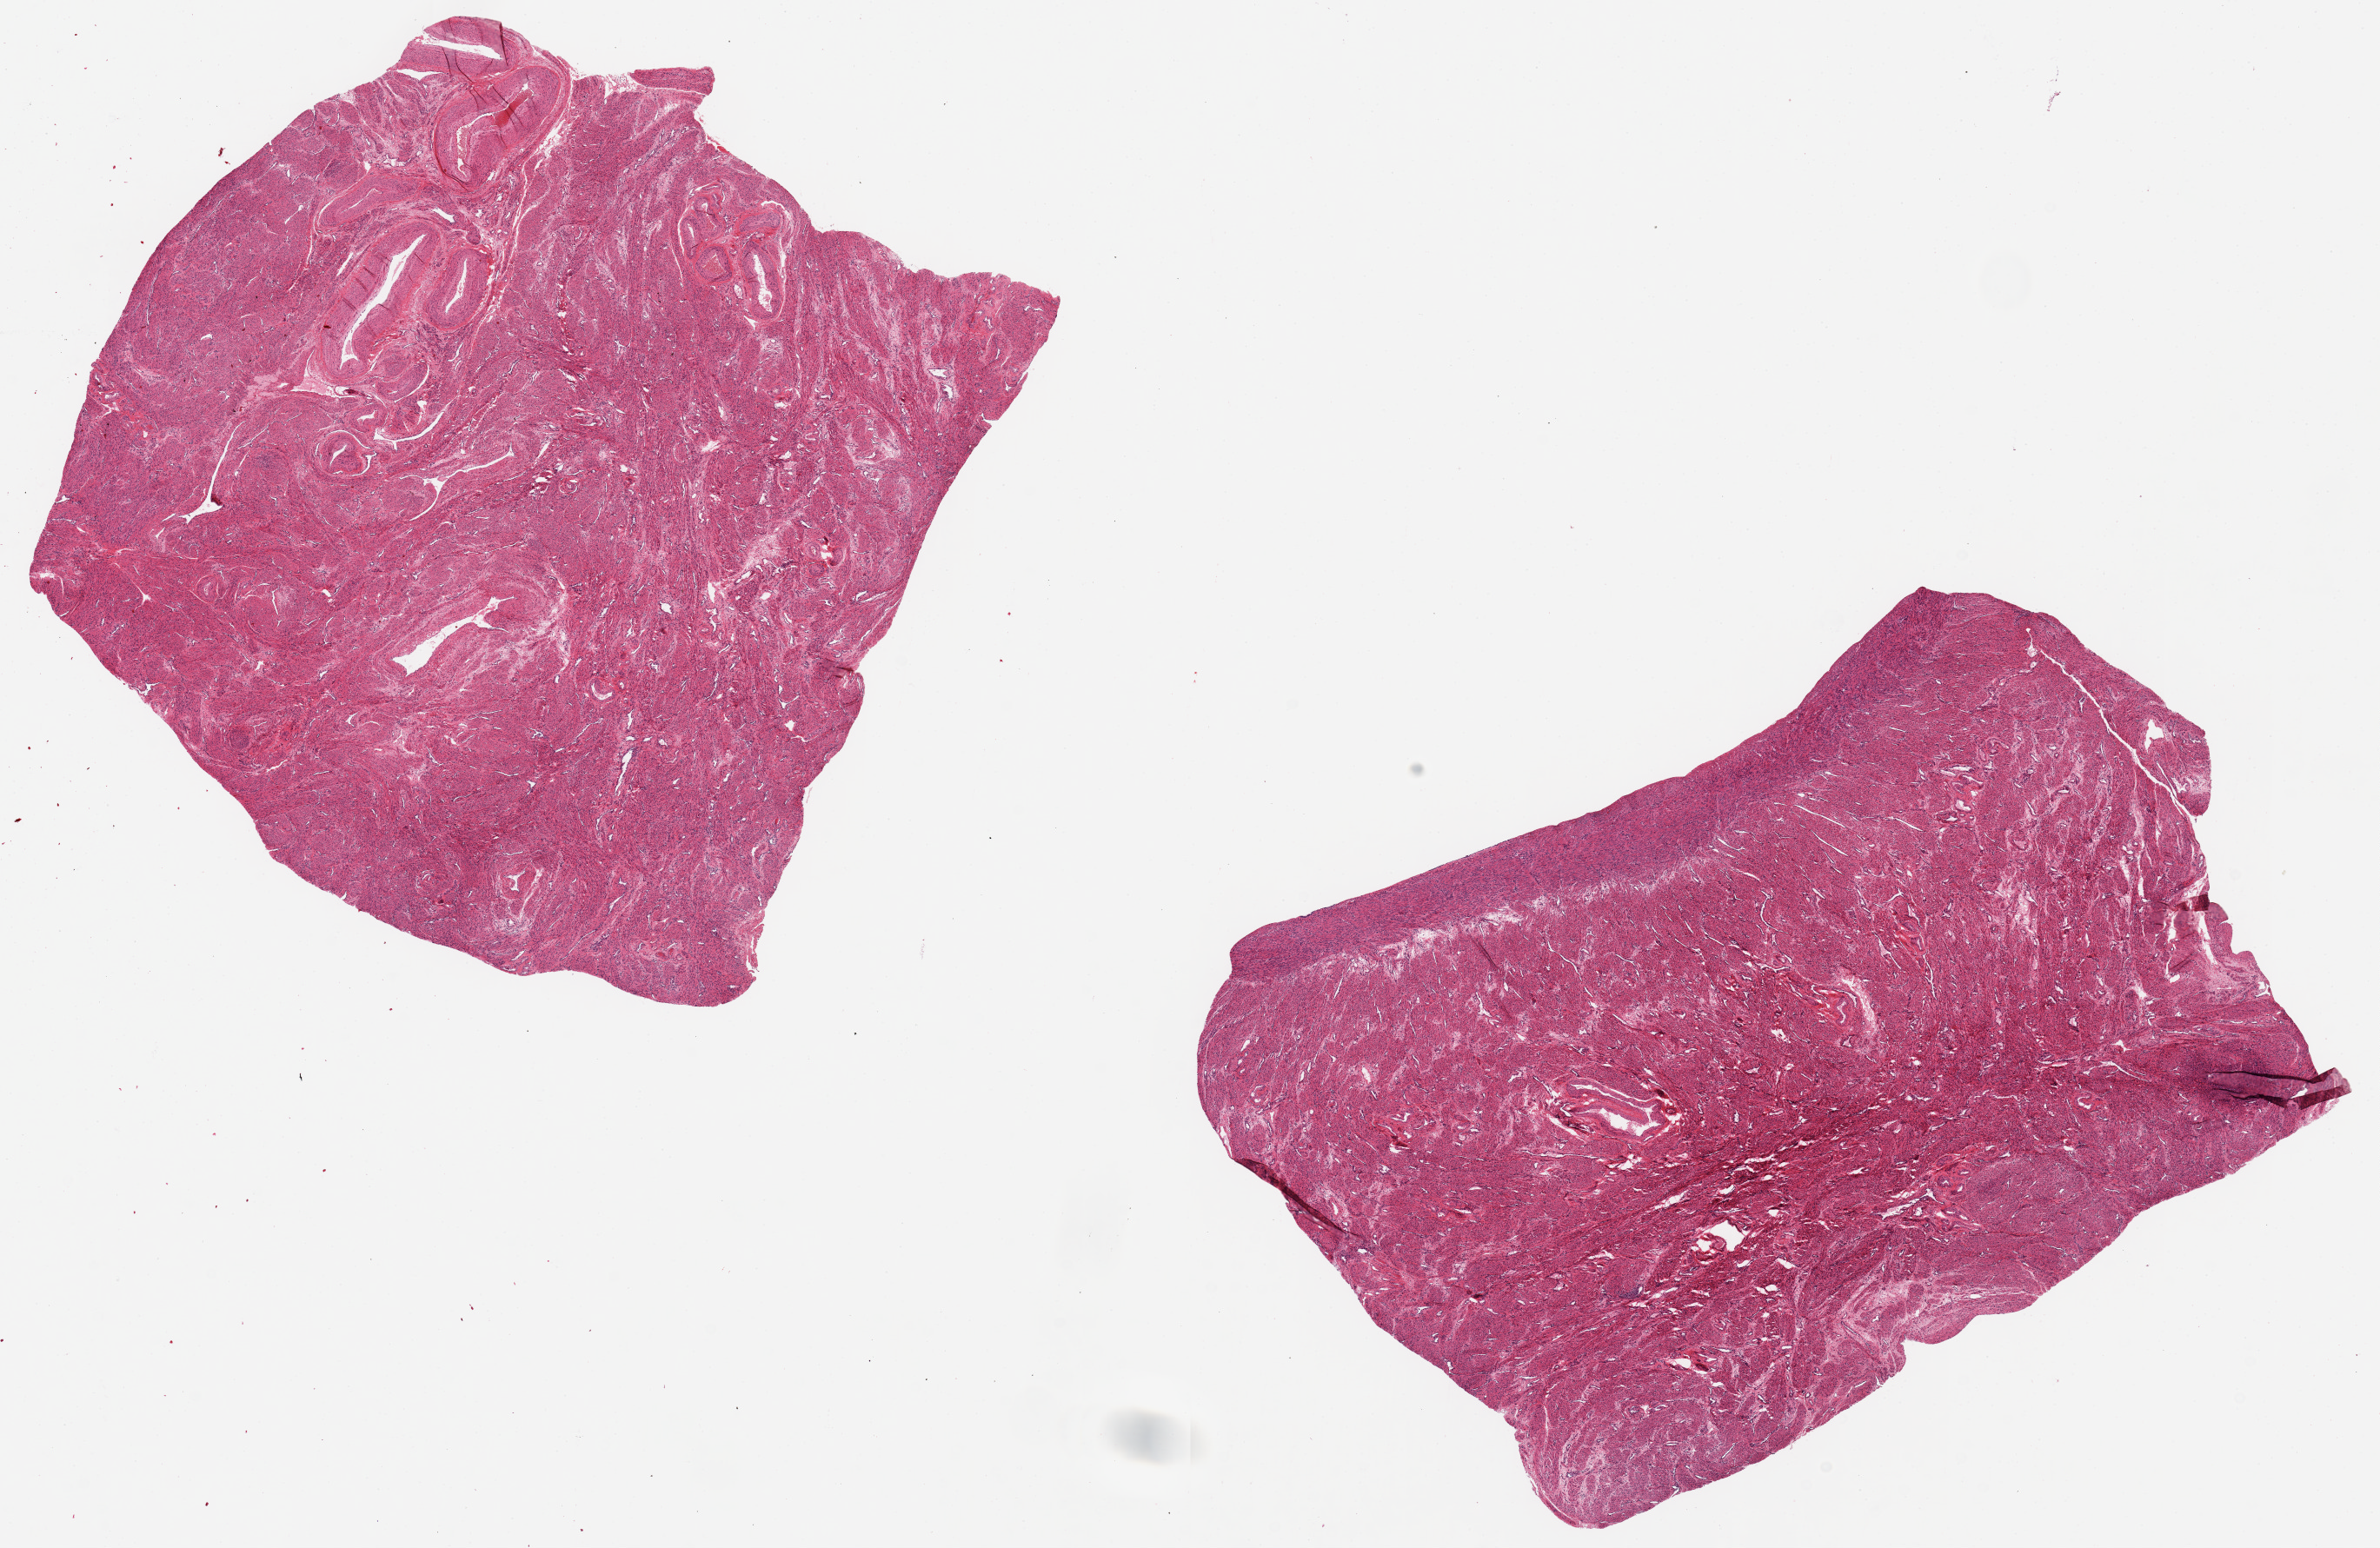
Hematoxylin and eosin (H&E) whole-slide image, brightfield, shown as a low-resolution overview of the whole scanned area (about 21.7 x 14.1 mm, acquisition: 20x scan). PAXgene-fixed, paraffin-embedded tissue. Sampled site (target tissue): uterus. Tissue donor sample. Female donor.
Pathologist's review note for this sample: 2 pieces, 8x8 & 10x6mm; all muscularis.